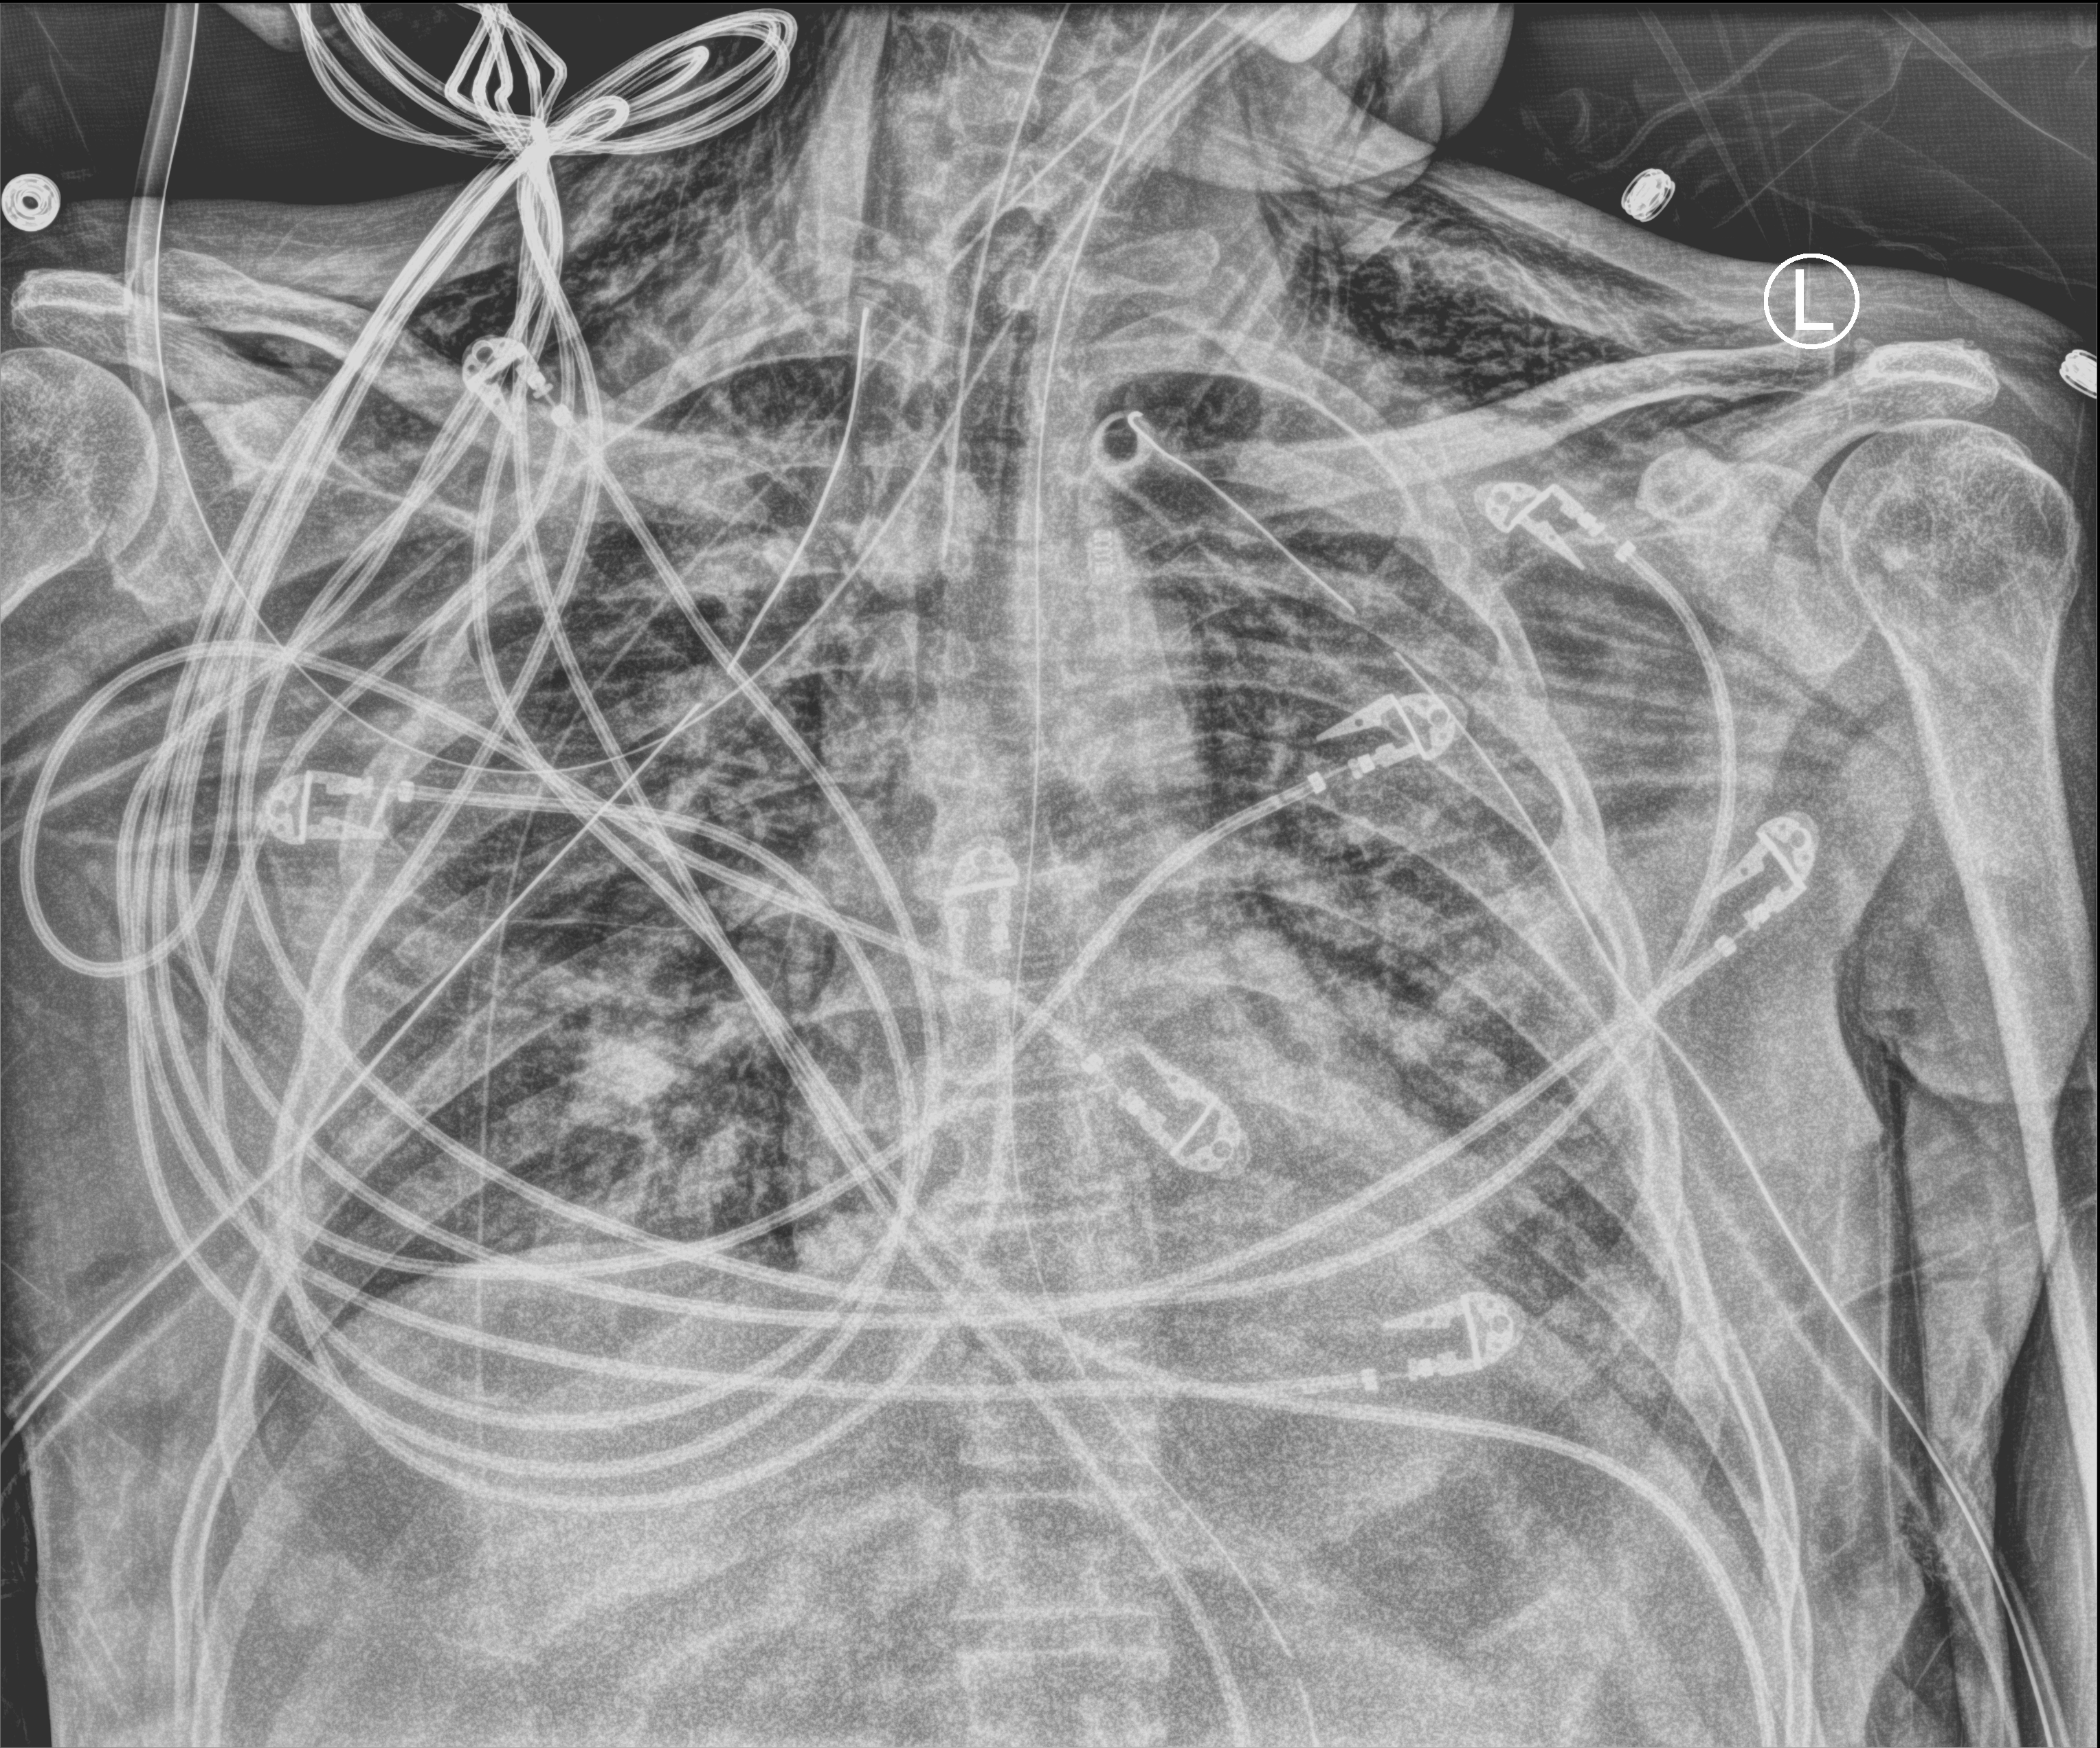
Portable chest radiograph; anteroposterior (AP) projection. Patient hospitalised with COVID-19; male, aged 18–59 years.
Hospital-stay facts (about this admission, not read from this image; timing relative to this image not recorded):
- chronic kidney disease (admission record): no
- admitted to intensive care during this hospital stay: yes
- mechanically ventilated during this hospital stay: yes